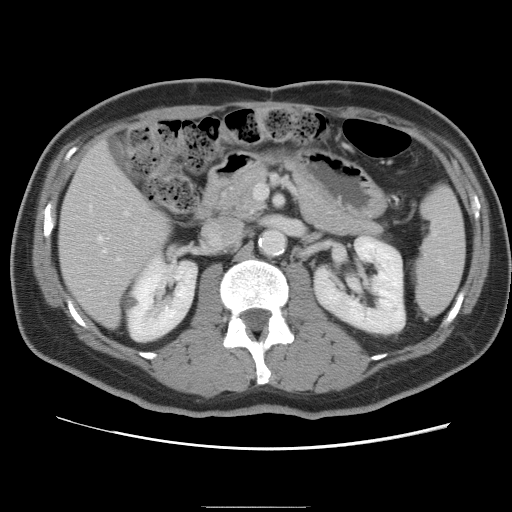
Contrast-enhanced abdominal CT, one axial slice; slice 37 of 87 in the series (ordered by position); 120 kVp; intravenous contrast given; soft-tissue window (W 400 / L 40 HU); 512 × 512 image matrix, field of view 363 × 363 mm. Male patient, age 63 years. Case-level facts recorded for this patient, not image findings: diagnosis: colorectal cancer liver metastases, imaged before liver resection; multiple liver metastases: no; largest metastasis: 9 cm; disease in both lobes: no.
Annotated regions visible in this slice (outlined manually by an expert reader):
- hepatic veins: bounding box (x1, y1, x2, y2) in pixels: (98, 236, 105, 252)
- liver: (60, 142, 169, 326)
- planned liver remnant (the part of the liver to remain after resection): (60, 142, 169, 327)
- portal vein (with intrahepatic branches): (102, 210, 130, 294)